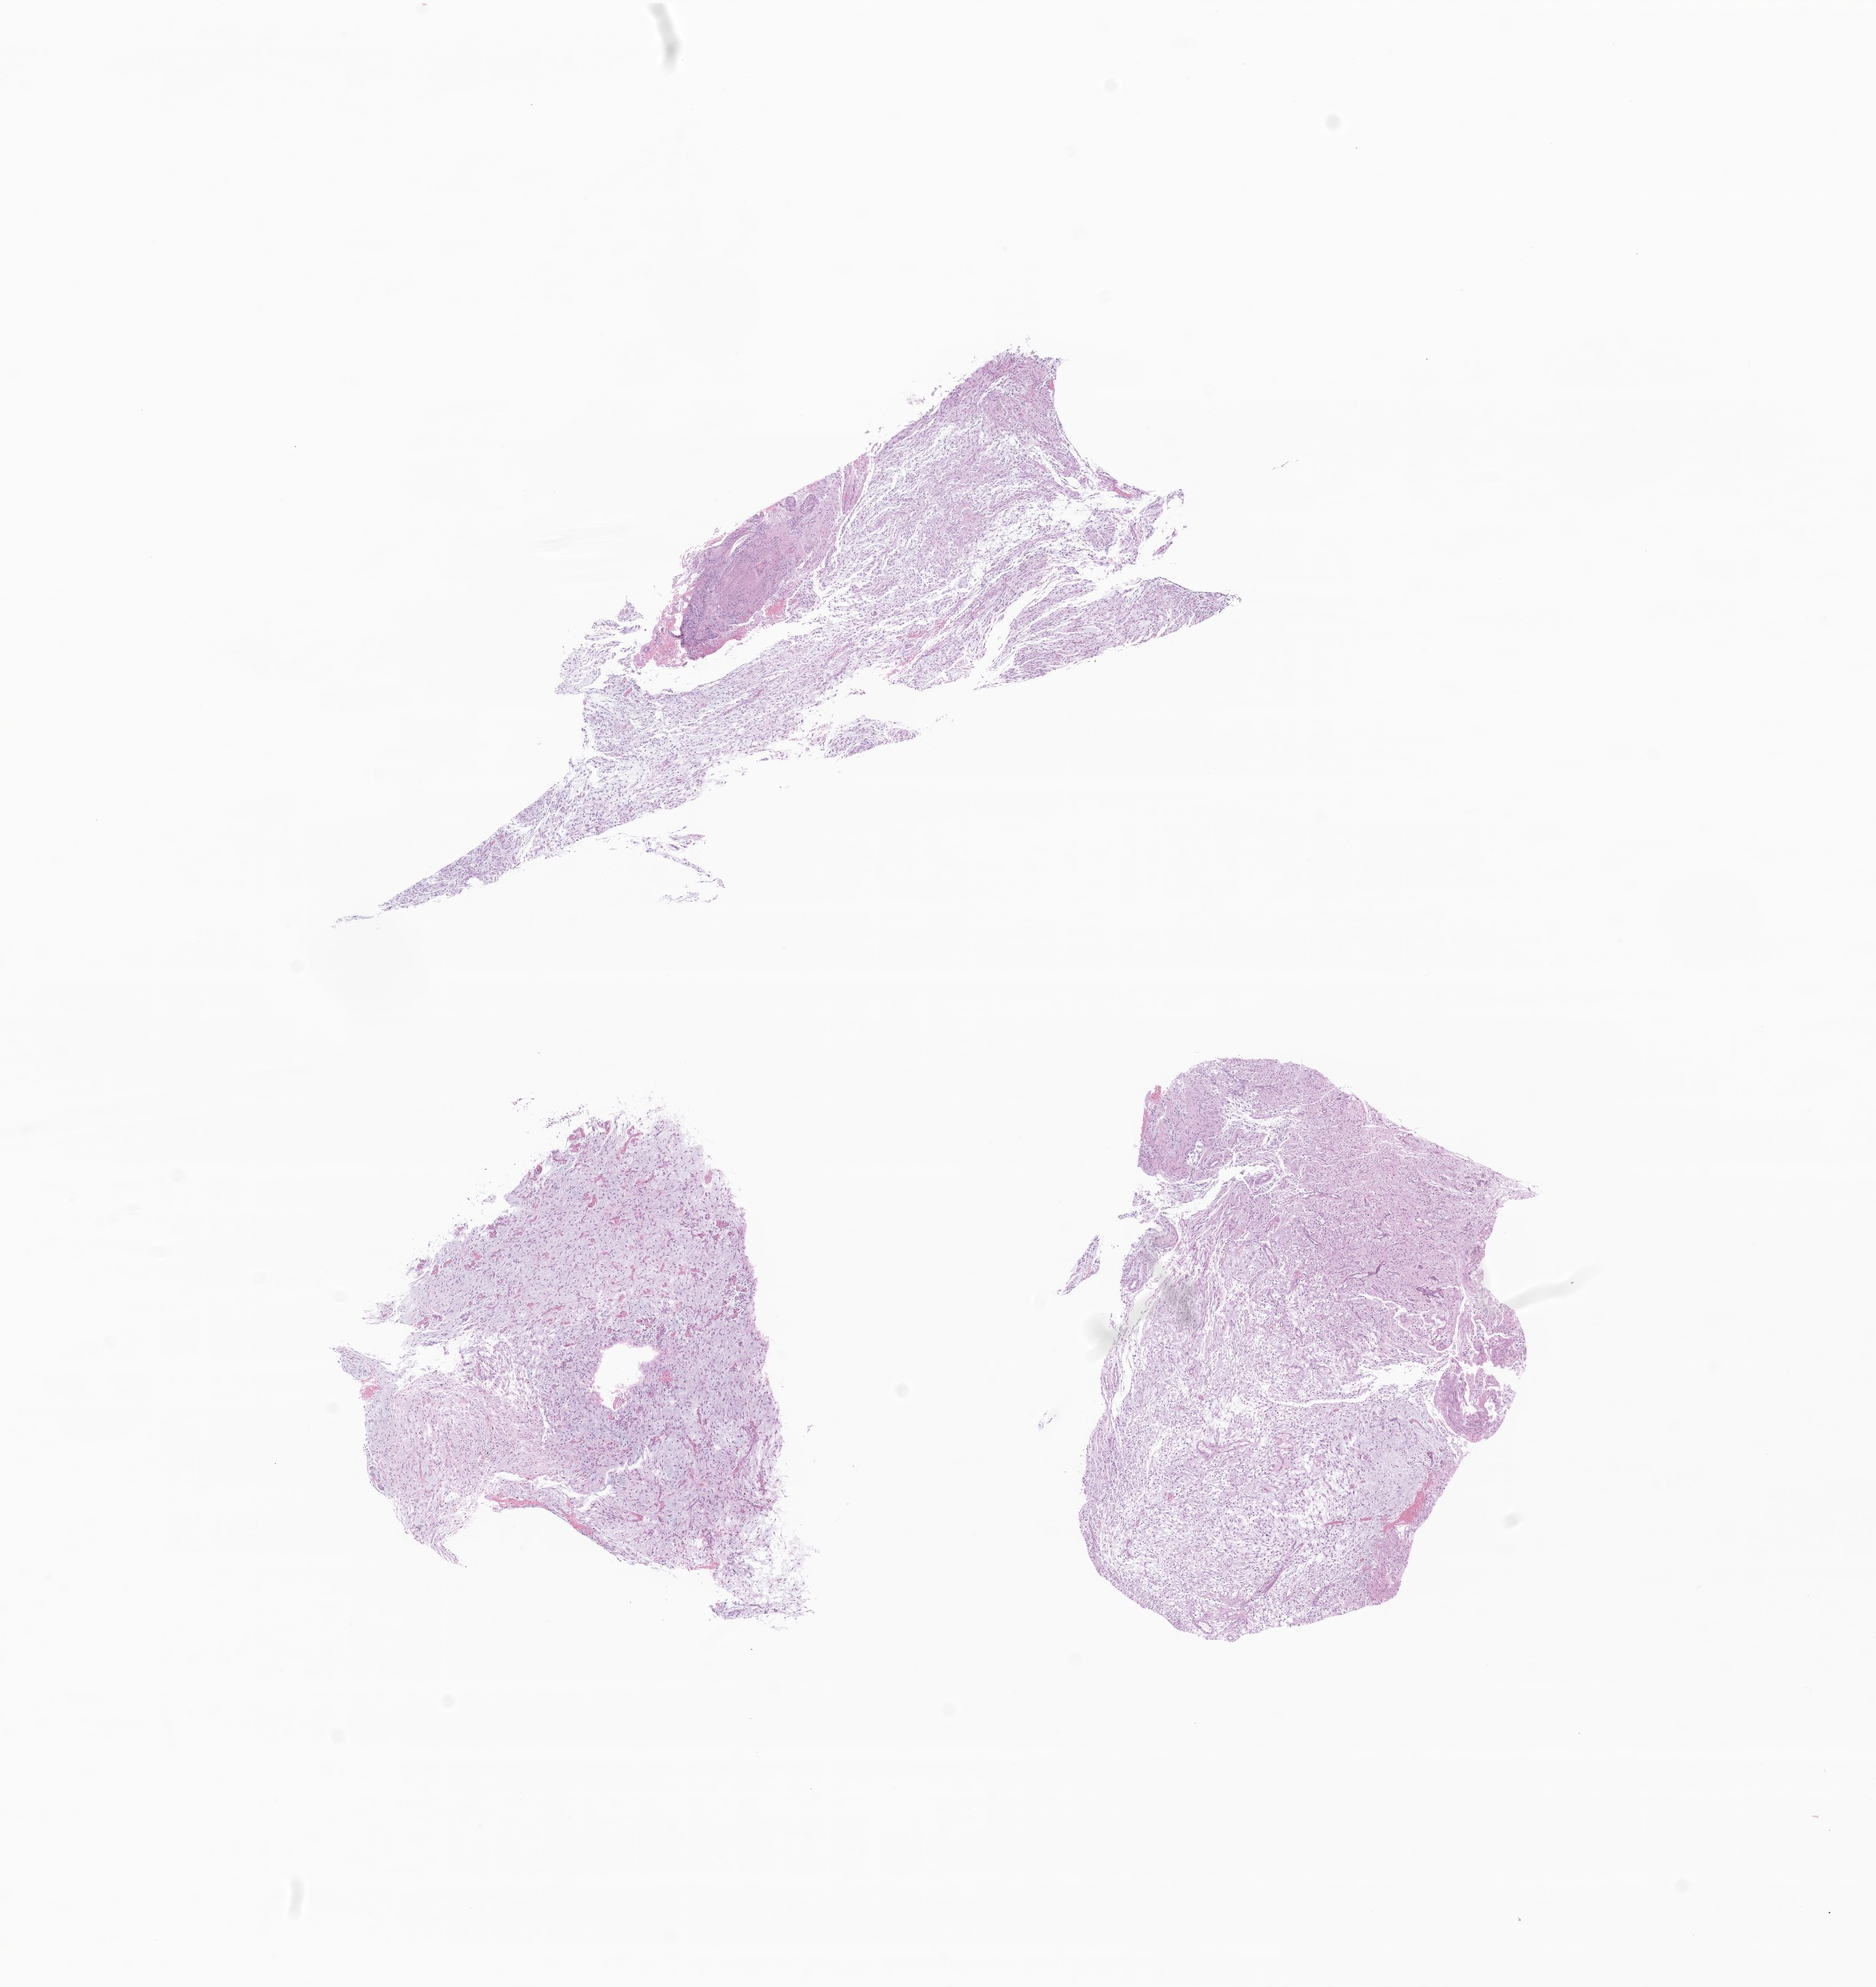
Whole-slide image, H&E stain of tumor tissue from the brain, a low-resolution overview of the entire scanned area, about 10.3 x 10.9 mm; formalin-fixed, paraffin-embedded (FFPE) tissue. Patient male; age 385 days (about 1.1 years).
* diagnosis (ICD-O-3 morphology term): Pilocytic astrocytoma